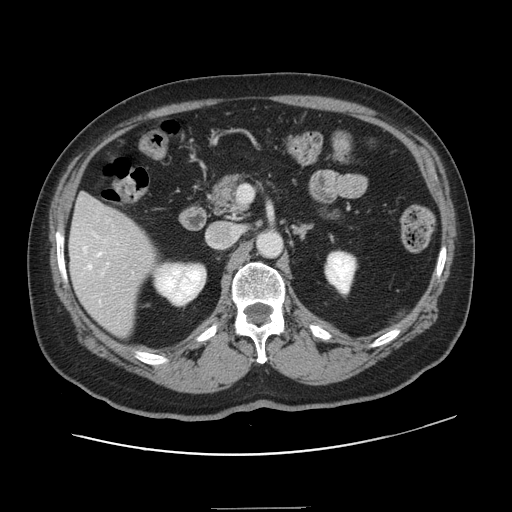
Contrast-enhanced abdominal CT, one axial slice. Position 70 of 143 along the scan axis. 120 kVp. Intravenous contrast given. Soft-tissue window (W 400 / L 40 HU). 512 × 512 image matrix, field of view 402 × 402 mm. Male patient, age 62 years. Case-level facts recorded for this patient, not image findings: diagnosis: colorectal cancer liver metastases, imaged before liver resection; multiple liver metastases: yes; largest metastasis: 2.7 cm; disease in both lobes: no.
Structures marked on this image (outlined manually by an expert reader):
- hepatic veins: bounding box (x1, y1, x2, y2) in pixels: (83, 247, 102, 269)
- liver: (70, 195, 157, 336)
- planned liver remnant (the part of the liver to remain after resection): (75, 195, 115, 219)
- portal vein (with intrahepatic branches): (104, 240, 109, 264)